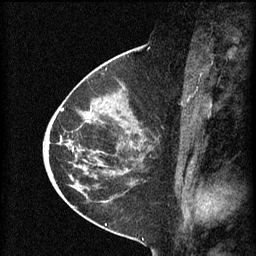
Breast MRI (dynamic contrast-enhanced), one sagittal slice. Slice 34 of 60 in the series (ordered by position). 3 images stored at this slice position (order not interpretable as contrast timing). 1.5 T. TE 4.2 ms, TR 8.2 ms. 2 mm slice thickness. 256 × 256 image matrix. Female patient, age 45 years.
Structures marked on this image (semi-automatic segmentation, software-assisted and operator-edited):
- analysis volume of interest (the breast-tissue region the enhancement analysis was run in; not a lesion): bounding box (x1, y1, x2, y2) in pixels: (80, 102, 152, 171)
- tumour enhancement mask (voxels above the 70 % enhancement threshold inside the analysis volume of interest): (87, 114, 91, 119)